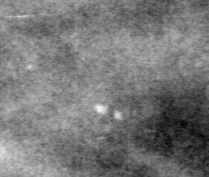
Cropped region of a digitized screen-film mammogram centred on a radiologist-marked abnormality; right breast; CC view; BI-RADS breast density category 2 (scale 1–4).
Marked abnormality: calcifications, morphology pleomorphic, distribution clustered; BI-RADS assessment category 3; subtlety rating 2 on a 1 (subtle) to 5 (obvious) scale; pathology result (as recorded, not read from the image): benign.